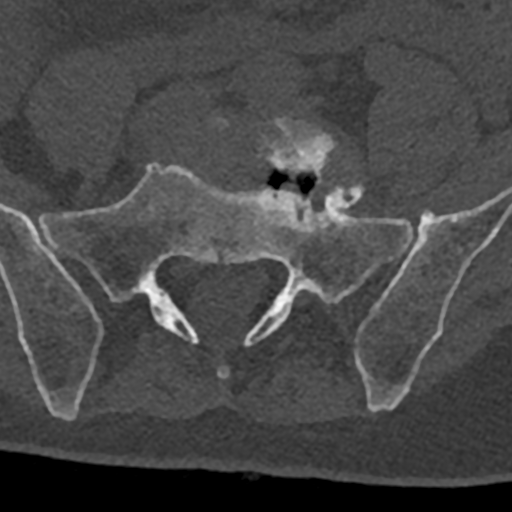
CT including the spine, one axial slice; position 154 of 797 along the scan axis; reconstruction kernel Br40s/3; bone window (W 1800 / L 400 HU); 0.5 mm slice thickness; 512 × 512 image matrix. Patient: male, 74 years. Case-level facts recorded for this patient, not image findings: primary cancer: renal; vertebrae with lytic lesions (as recorded): T10, L1, L2, L3, L4, L5.
Annotated regions visible in this slice (semi-automatic segmentation, software-assisted and operator-edited):
- L5 vertebra: bounding box <216,117,337,185> (left, top, right, bottom; pixels)